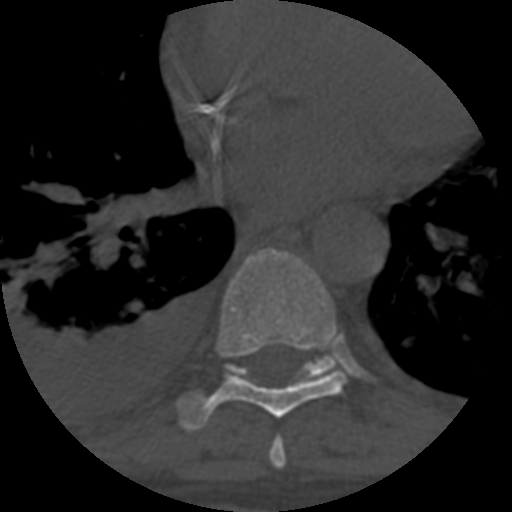
CT including the spine, one axial slice. Slice 394 of 708 in the series (ordered by position). Reconstruction kernel STANDARD. One of 3 acquisitions stored at this slice position. Bone window (W 1800 / L 400 HU). 1.25 mm slice thickness. 512 × 512 image matrix, field of view 160 × 160 mm. Patient age 55 years. From the clinical record (not read from this slice): primary cancer: colon.
Outlined on this slice (semi-automatic segmentation, software-assisted and operator-edited):
- T7 vertebra: bounding box (x1, y1, x2, y2) in pixels: (269, 437, 286, 467)
- T8 vertebra: (178, 248, 347, 431)
- T9 vertebra: (226, 355, 345, 381)